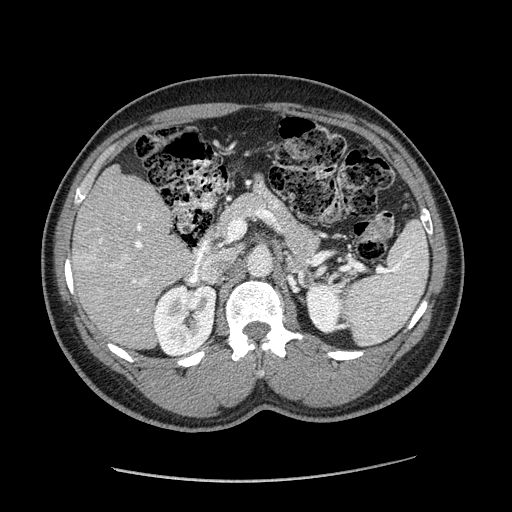
Contrast-enhanced abdominal CT (liver protocol), one axial slice; slice 89 of 182 in the series (ordered by position); reconstruction kernel STANDARD; 120 kVp; soft-tissue window (W 400 / L 40 HU); 512 × 512 image matrix. From the clinical record (not read from this slice): diagnosis: hepatocellular carcinoma (patient treated with transarterial chemoembolisation; whether this scan precedes or follows treatment is not stated here); TNM stage (as recorded): Stage-I; Child-Pugh class: A; tumour differentiation: well differentiated; tumour nodularity: uninodular.
Outlined on this slice (semi-automatically segmented with operator editing):
- liver parenchyma outside the tumour (the mass and vessels are separate outlines, so this box may not span the whole liver): bounding box [x1, y1, x2, y2] px = [71, 164, 192, 348]
- mass: [86, 223, 130, 270]
- liver vessels: [89, 218, 147, 311]